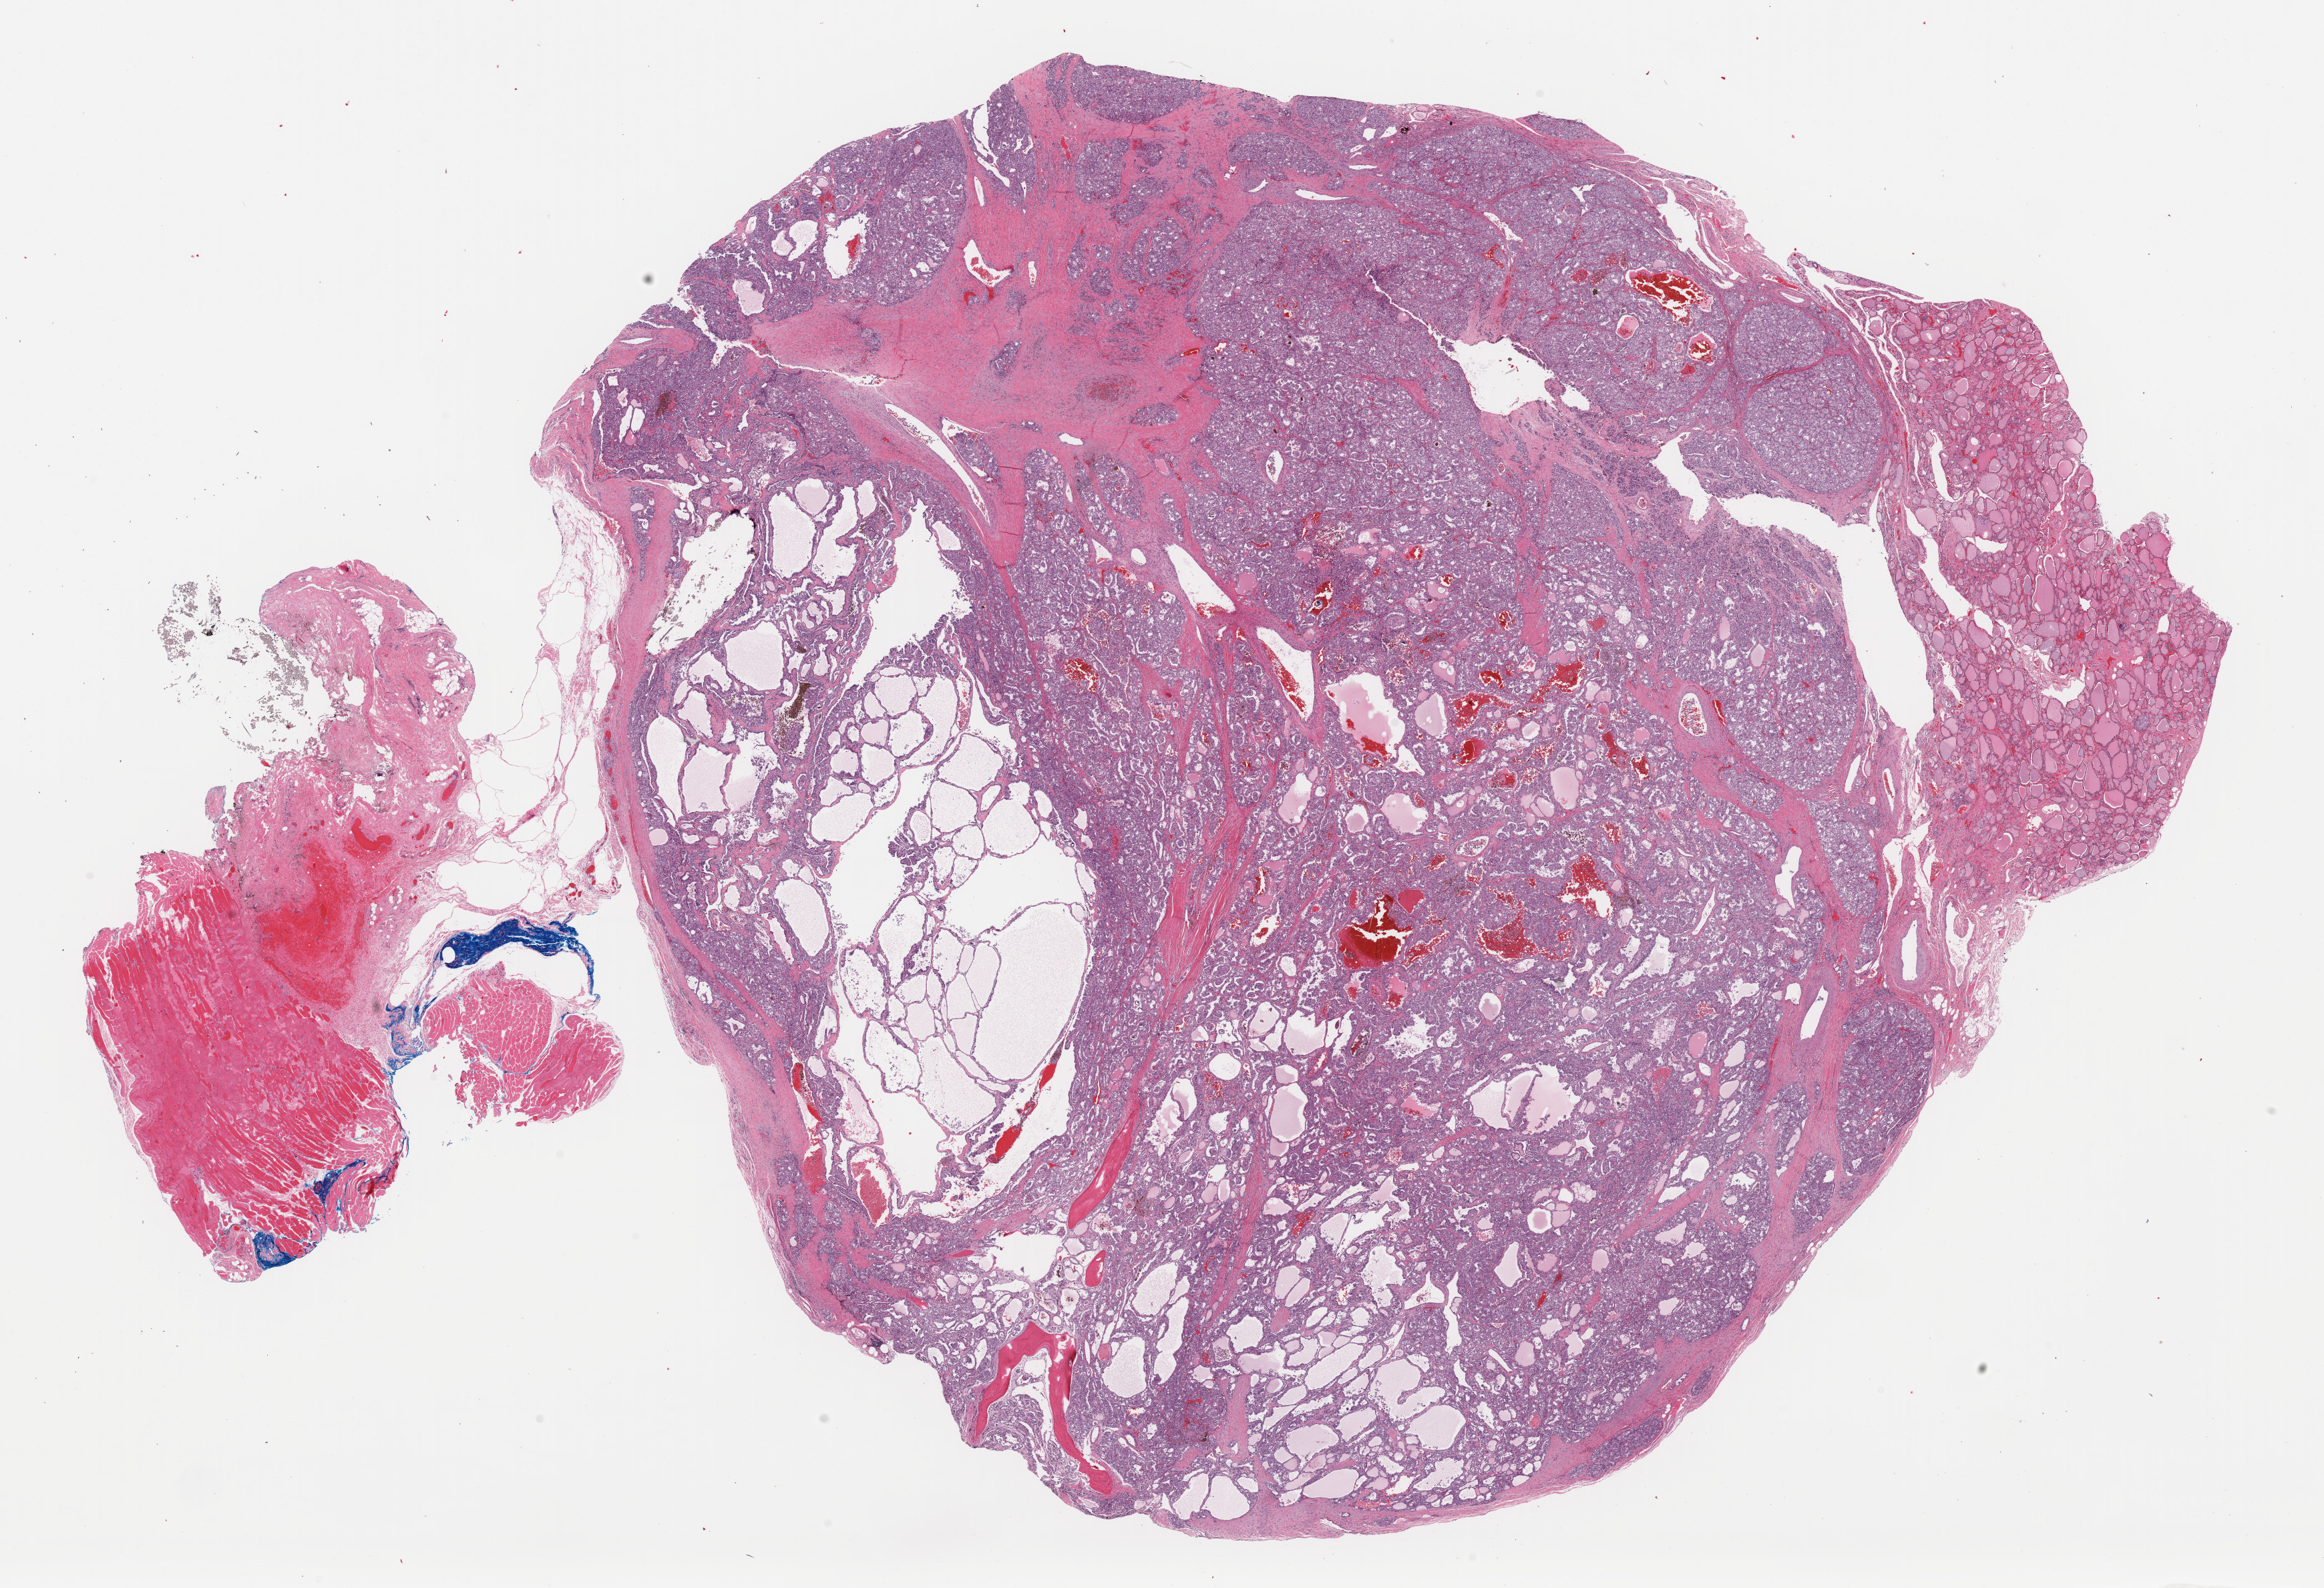
Whole-slide histology image, H&E — whole scanned area (about 27.5 x 18.8 mm) shown as a low-resolution overview; FFPE section; sample: primary tumour, thyroid. Patient: male, age at initial diagnosis 63 years.
Diagnosis: Papillary adenocarcinoma, NOS (thyroid gland). Lymph nodes positive (case pathology): 6 of 25 examined. AJCC pathologic stage: IVA (7th edition). Laterality: bilateral.